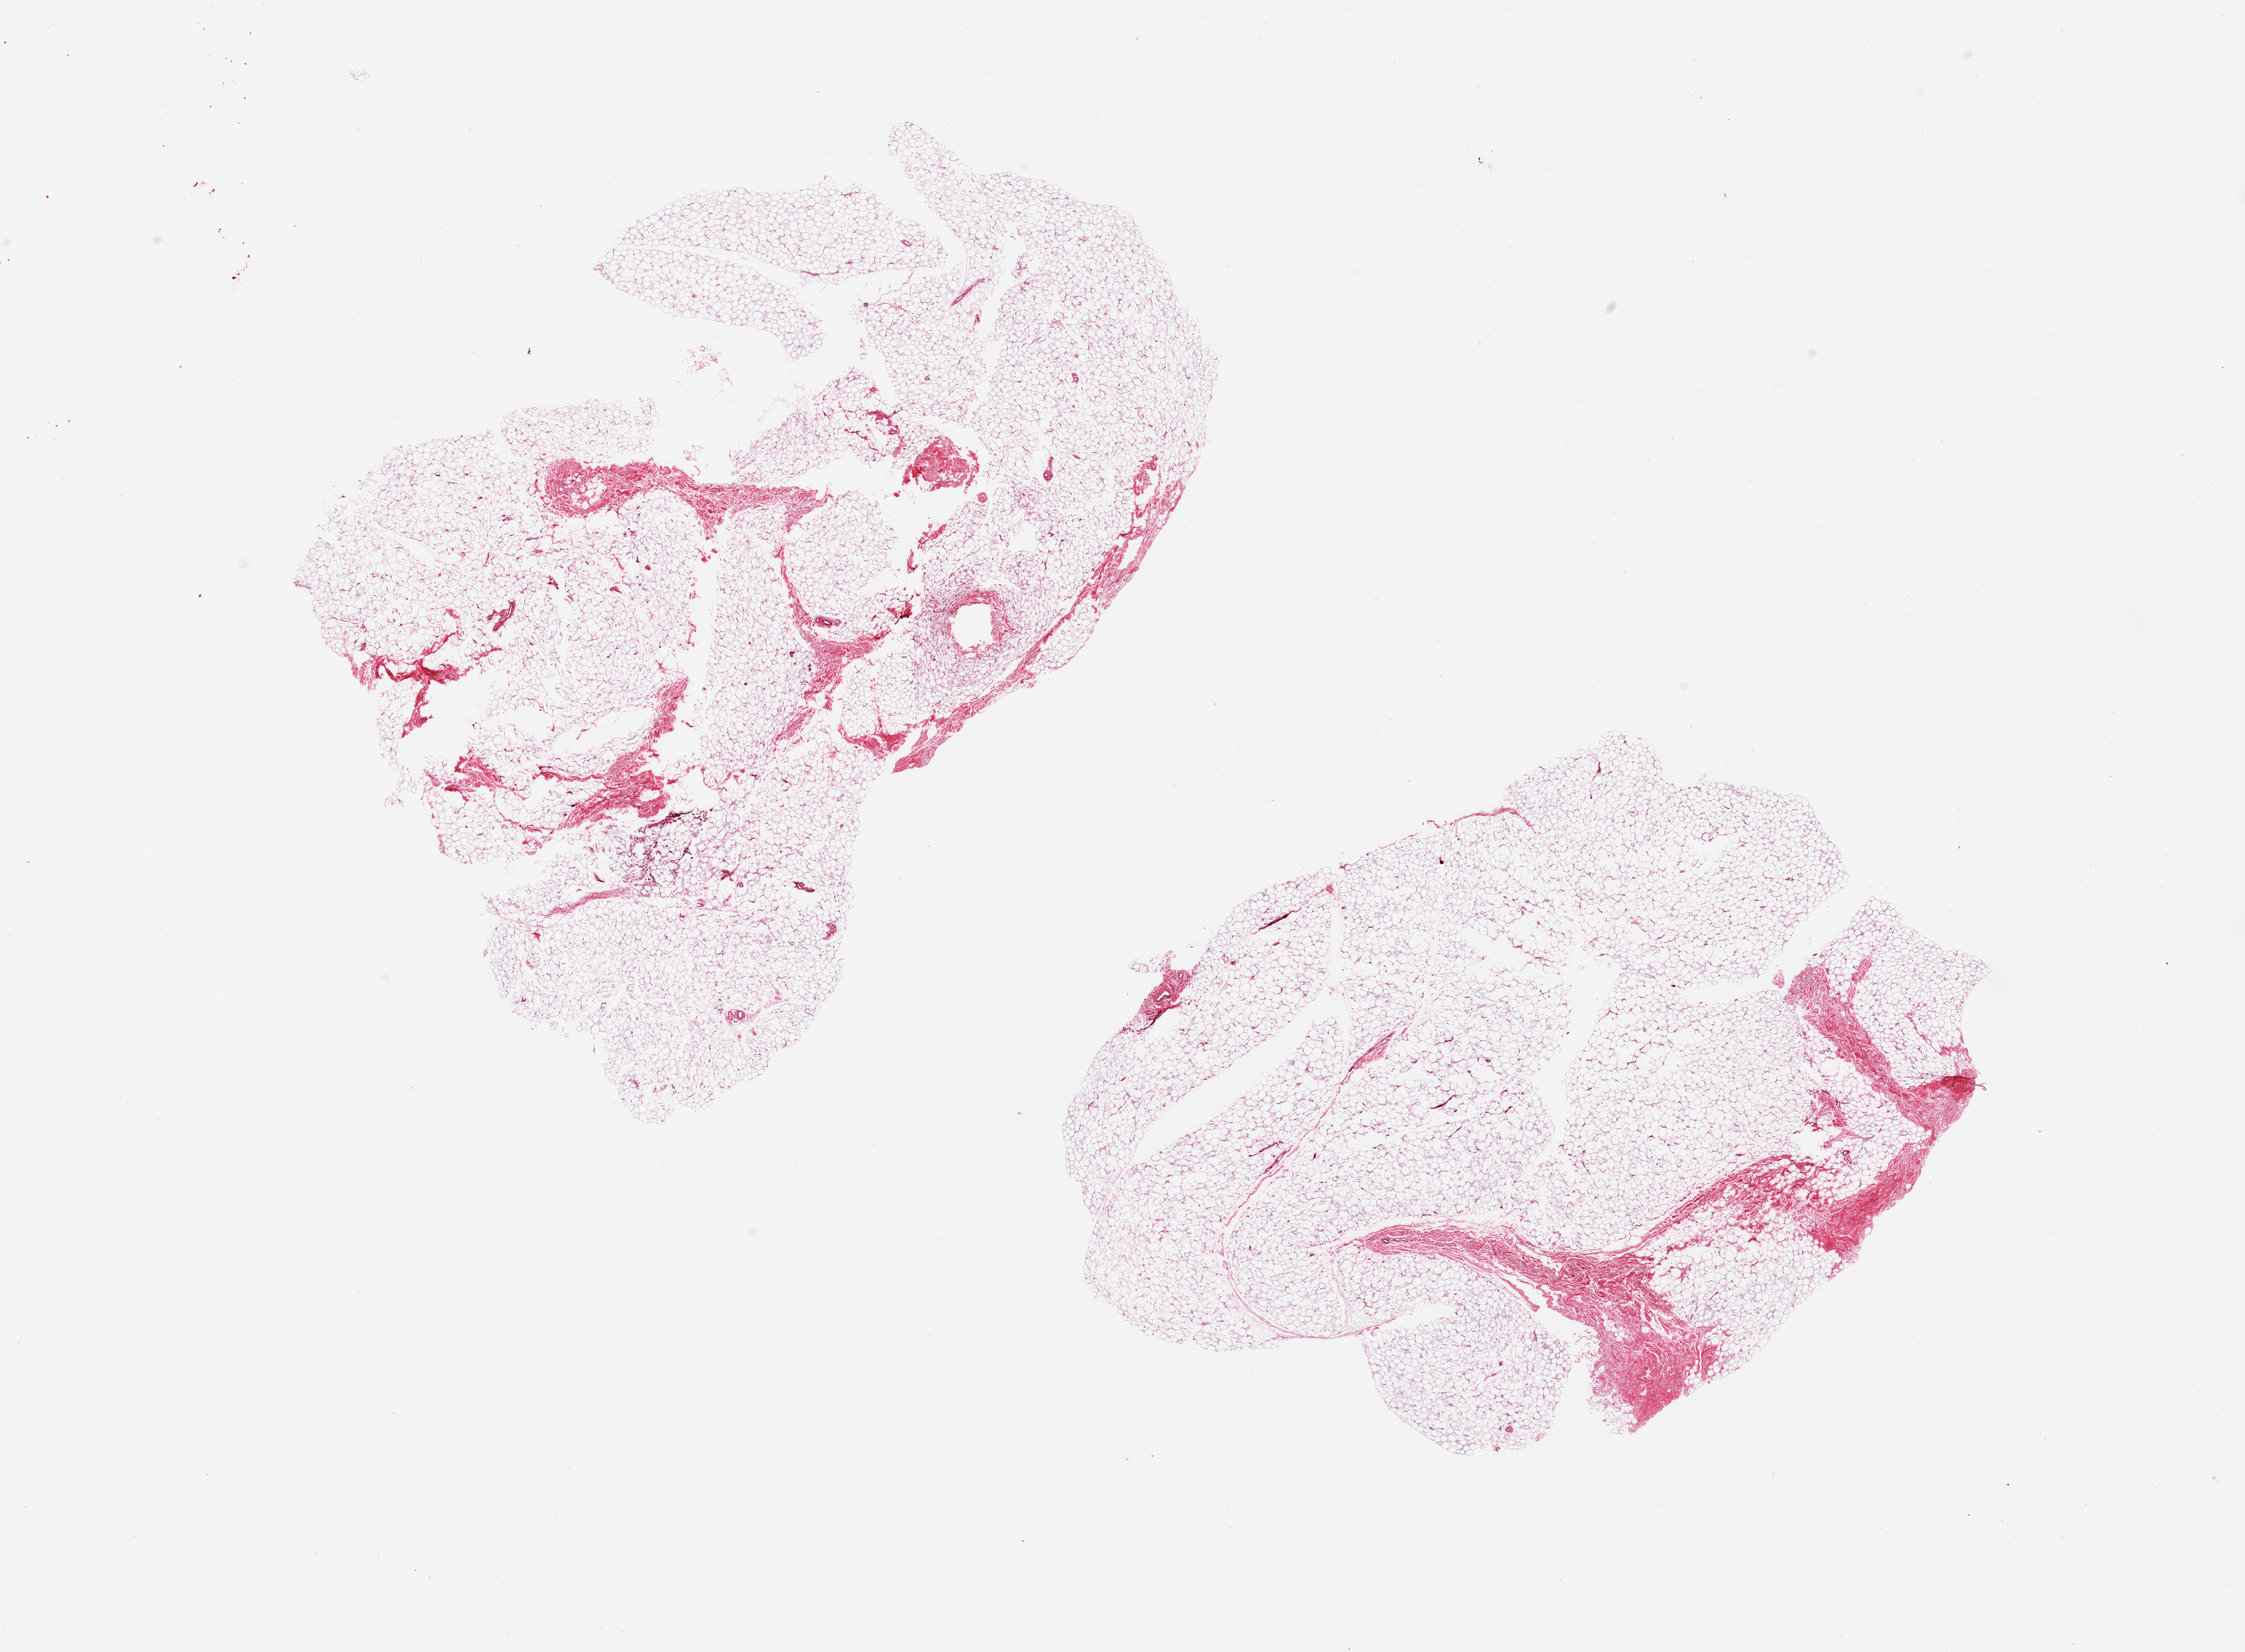
Whole-slide image, haematoxylin and eosin stain — low-resolution overview of the scanned area, about 24.6 x 18.1 mm, PAXgene-fixed, paraffin-embedded tissue, sampled site (target tissue): adipose tissue, donor tissue sample. Donor sex: male.
Reviewer comment on this tissue sample: 2 piece; mature adipose tissue and fibrovascular components.